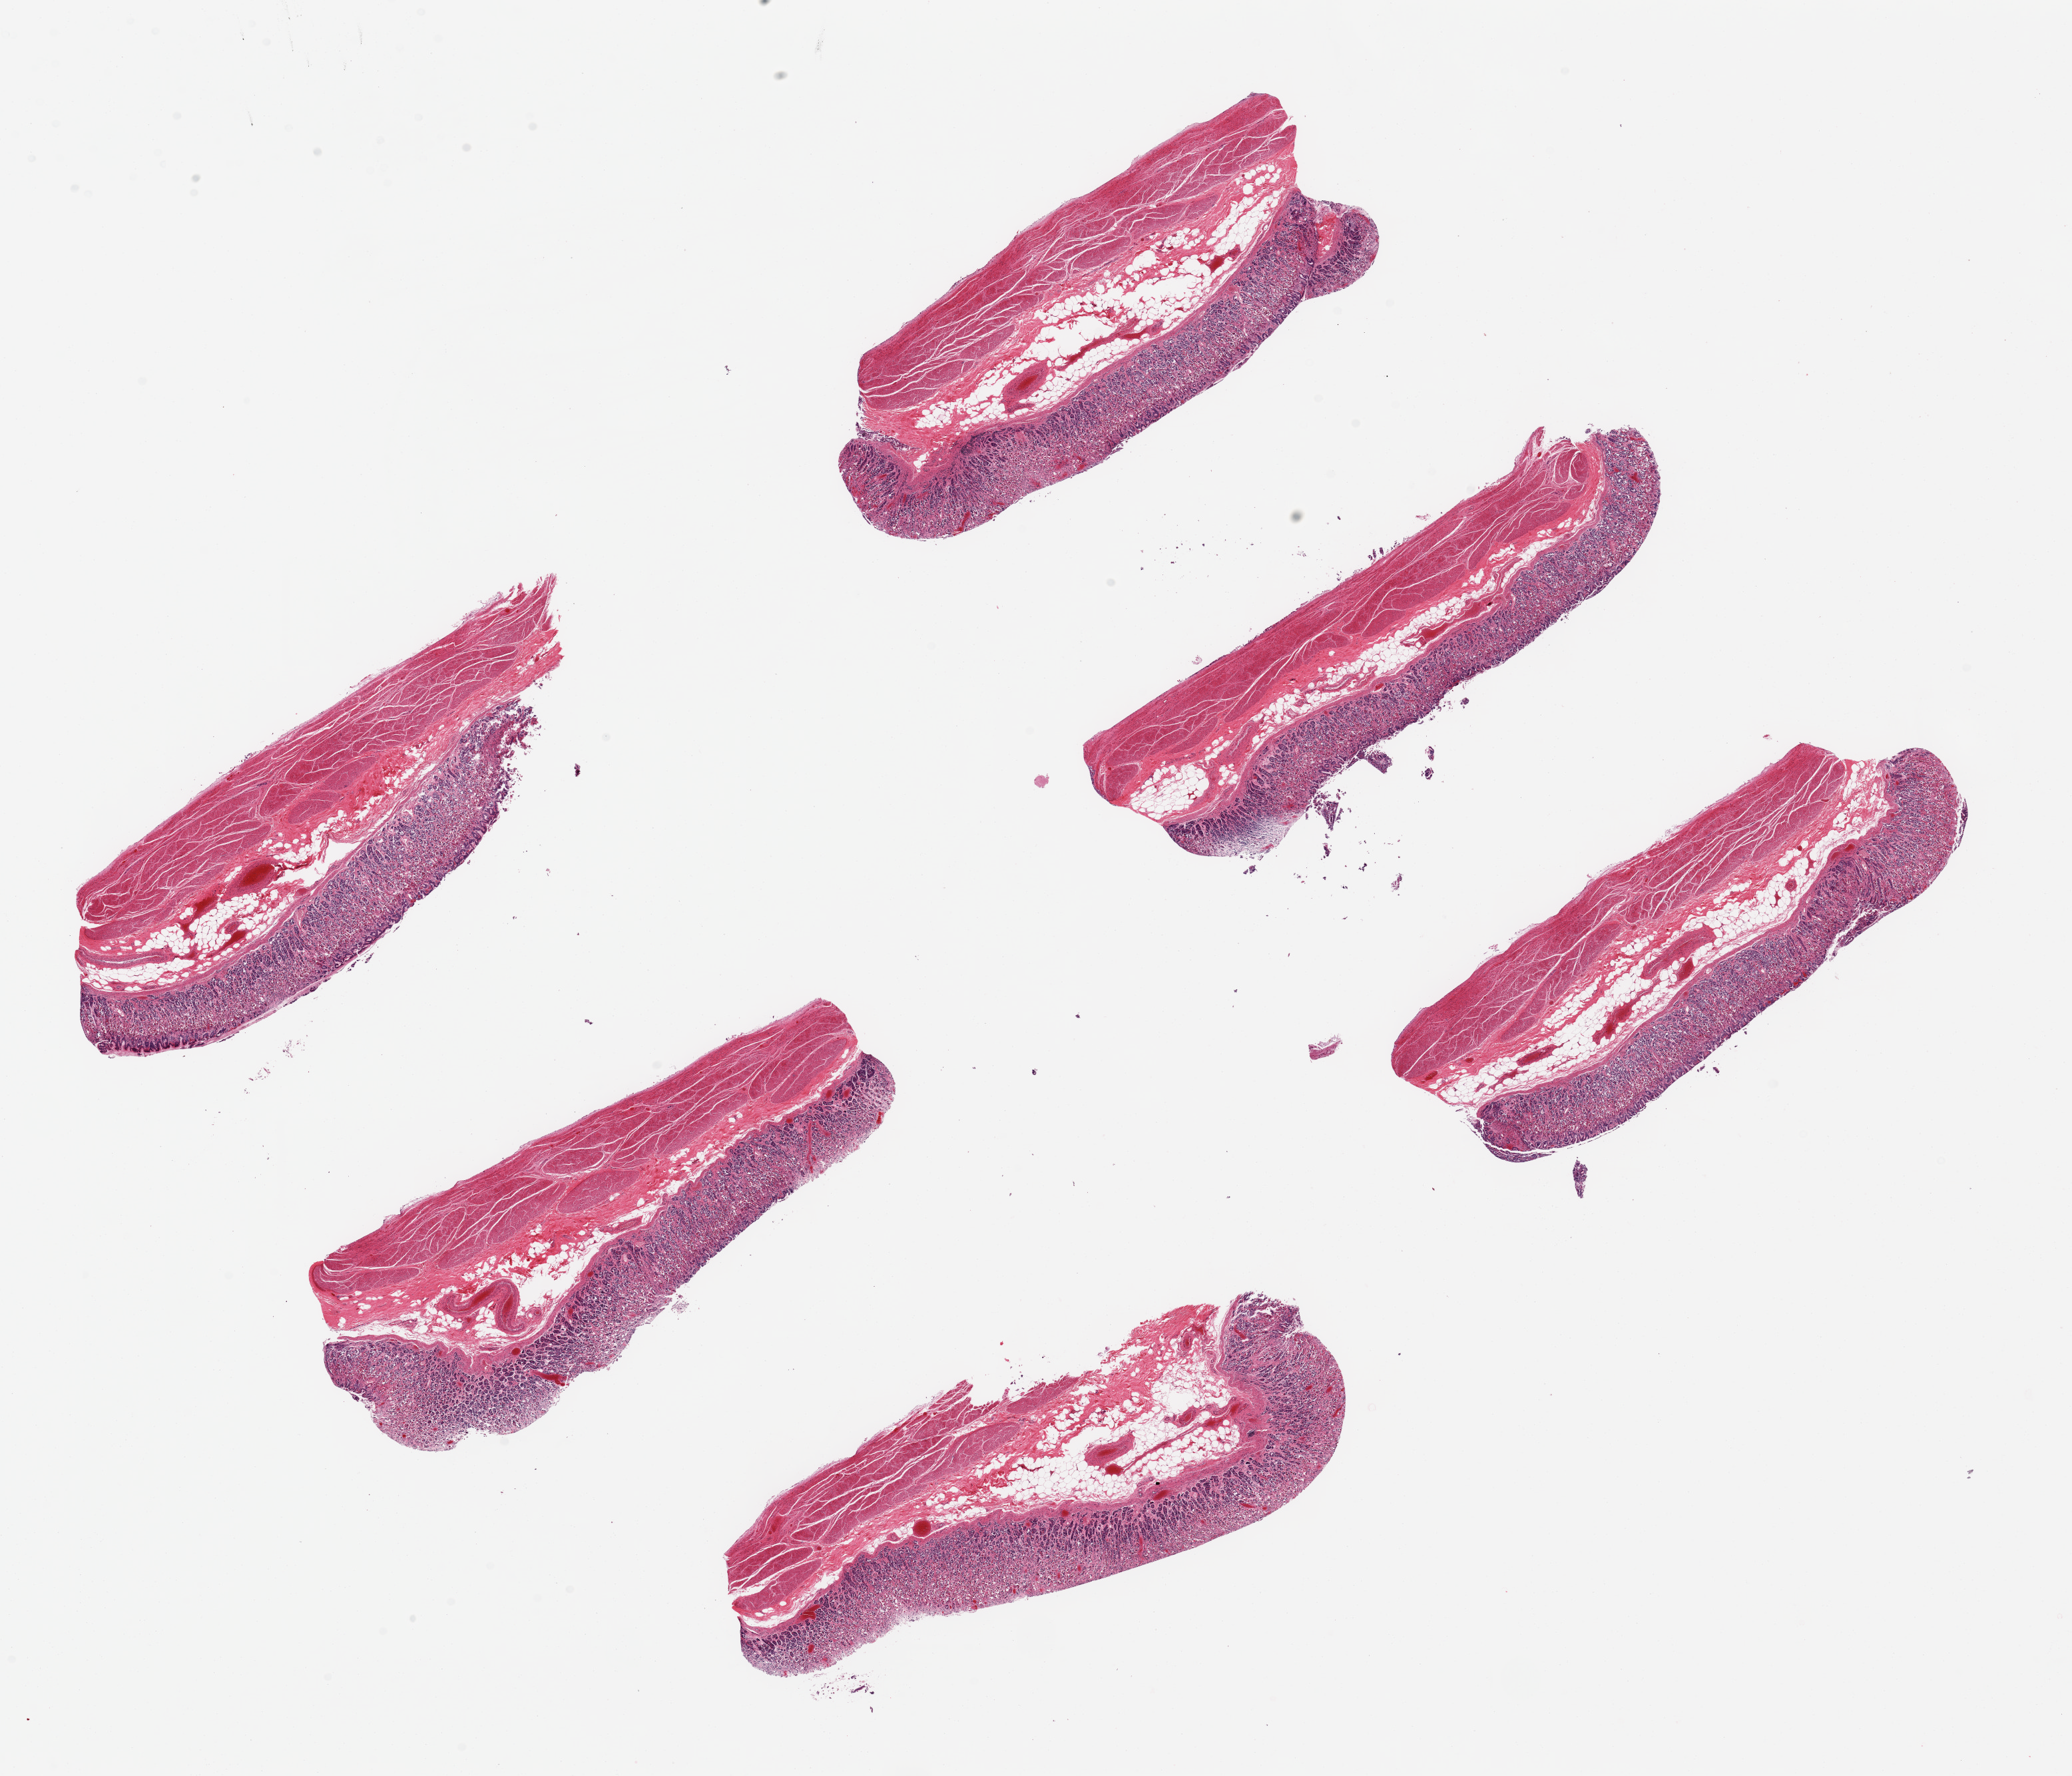
Whole-slide image, hematoxylin and eosin (H&E) stain — shown as a low-resolution overview of the whole scanned area (about 24.6 x 21.1 mm, from a 20x scan). PAXgene-fixed paraffin-embedded (PFPE) section. Section of stomach (target tissue). Tissue donor sample. Donor sex: male.
Reviewer comment on this tissue sample: 6 pieces,~7.5x2.5mm; mucosa 0.8mm.